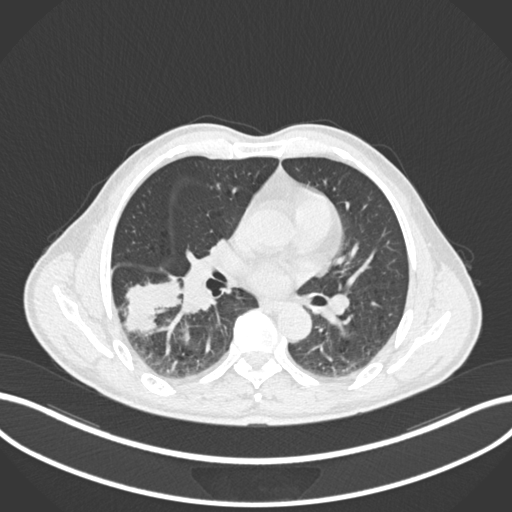
Chest CT, one axial slice; slice 100 of 208 in the series (ordered by position); 120 kVp; lung window (W 1500 / L -600 HU); 1 mm slice thickness; 512 × 512 image matrix, field of view 400 × 400 mm. Male patient, age 58 years. From the clinical record (not read from this slice): clinical TNM (as recorded): T3 N0 M0; histopathological grade: G2.
Outlined on this slice (bounding box drawn by a radiologist):
- lung tumour (recorded histology: squamous cell carcinoma): bounding box (x1, y1, x2, y2) in pixels: (122, 269, 183, 338)